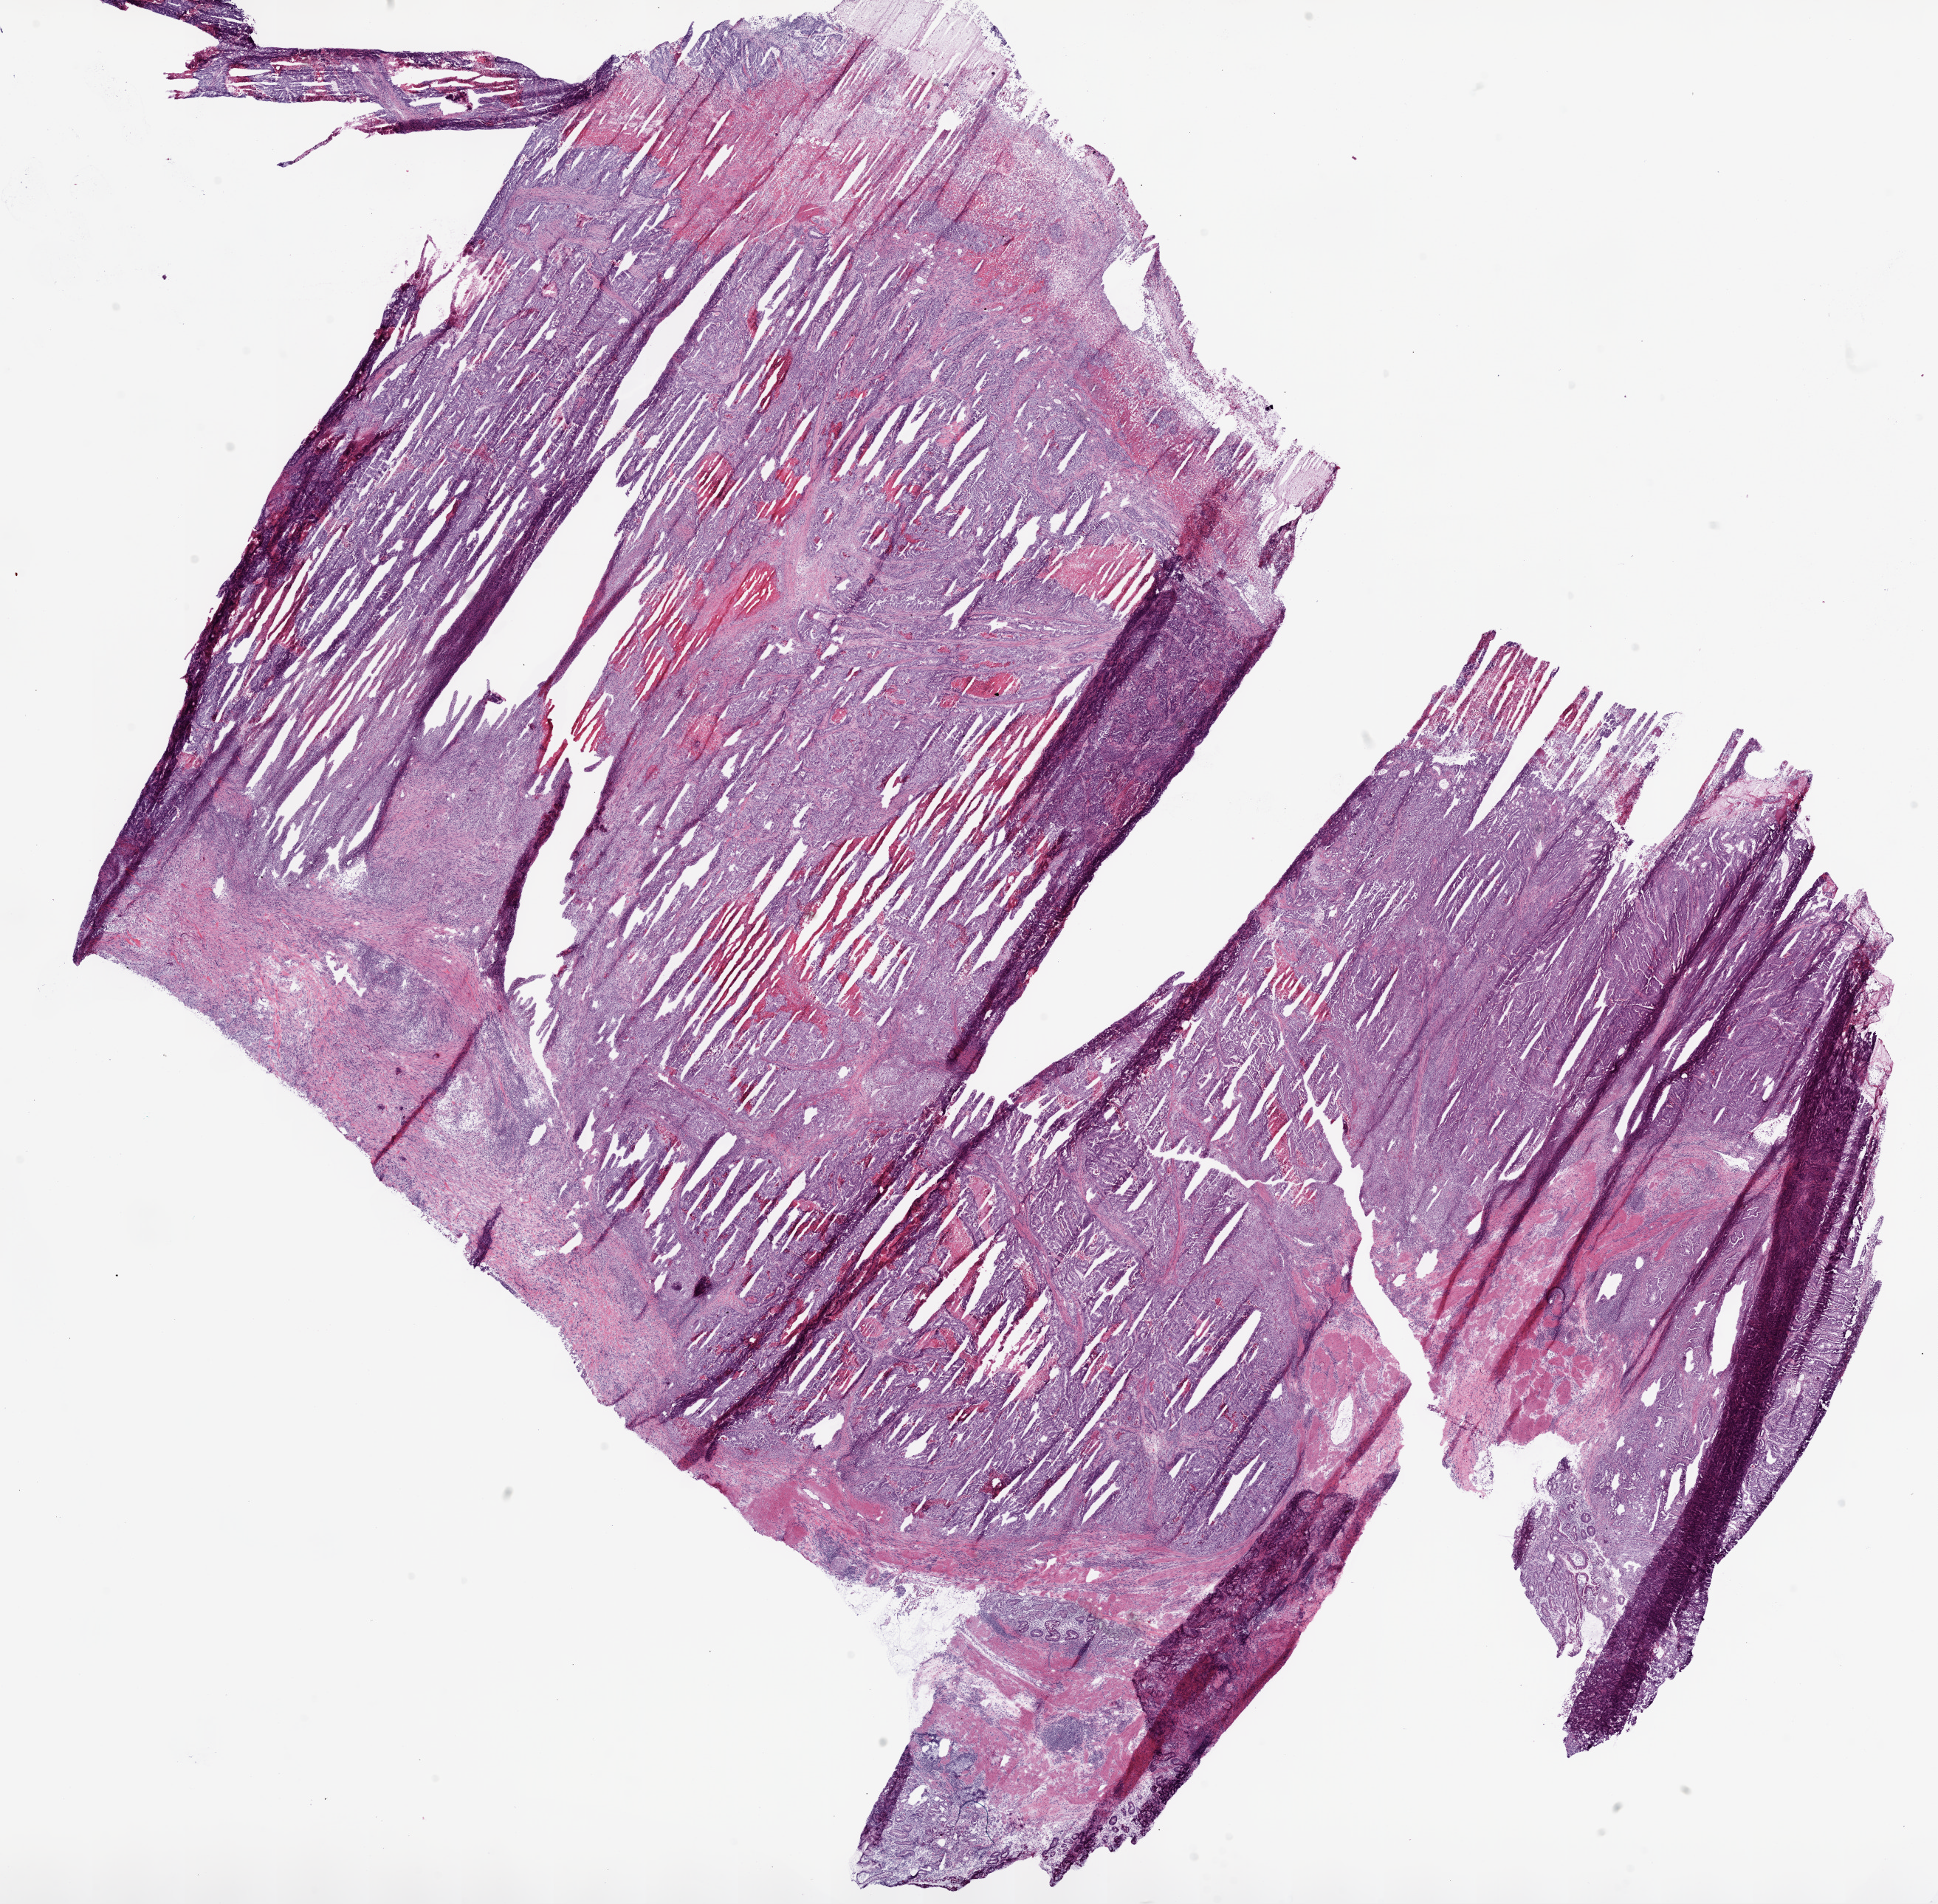
Whole-slide histology image, Hematoxylin and eosin (H&E) stained, low-resolution overview of the scanned area, about 21.1 x 20.7 mm (slide scanned at 20x), frozen section from the bottom of the tissue portion, stomach, primary tumour sample. Male patient; age at initial diagnosis 58 years. Composition of this section per pathologist review: tumour cells 80%, tumour nuclei 70%.
Pathologic diagnosis: Adenocarcinoma, NOS (body of stomach).